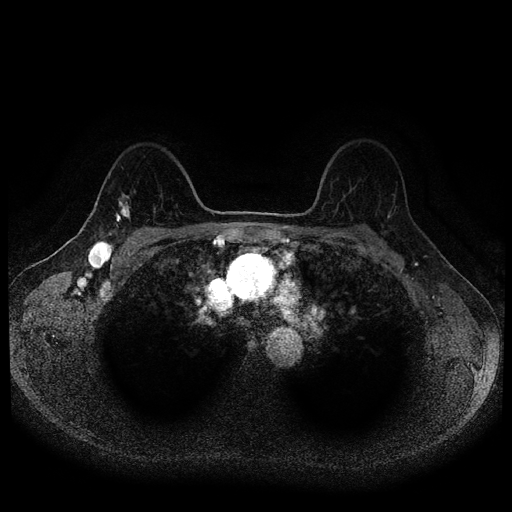
Breast MRI (dynamic contrast-enhanced, multi-phase), one axial slice; dynamic contrast-enhanced series, time point 2 of 5 at this slice position (early post-contrast); 1.5 T; TE 2.6 ms, TR 5.4 ms; 2 mm slice thickness; 512 × 512 image matrix, field of view 340 × 340 mm. Female patient, age 49 years.
Structures marked on this image (semi-automatic segmentation, software-assisted and operator-edited):
- breast lesion (labelled 'tumour' in the annotation; benign lesions carry a separate 'benign' label): box from (x=111, y=191) to (x=132, y=235) px